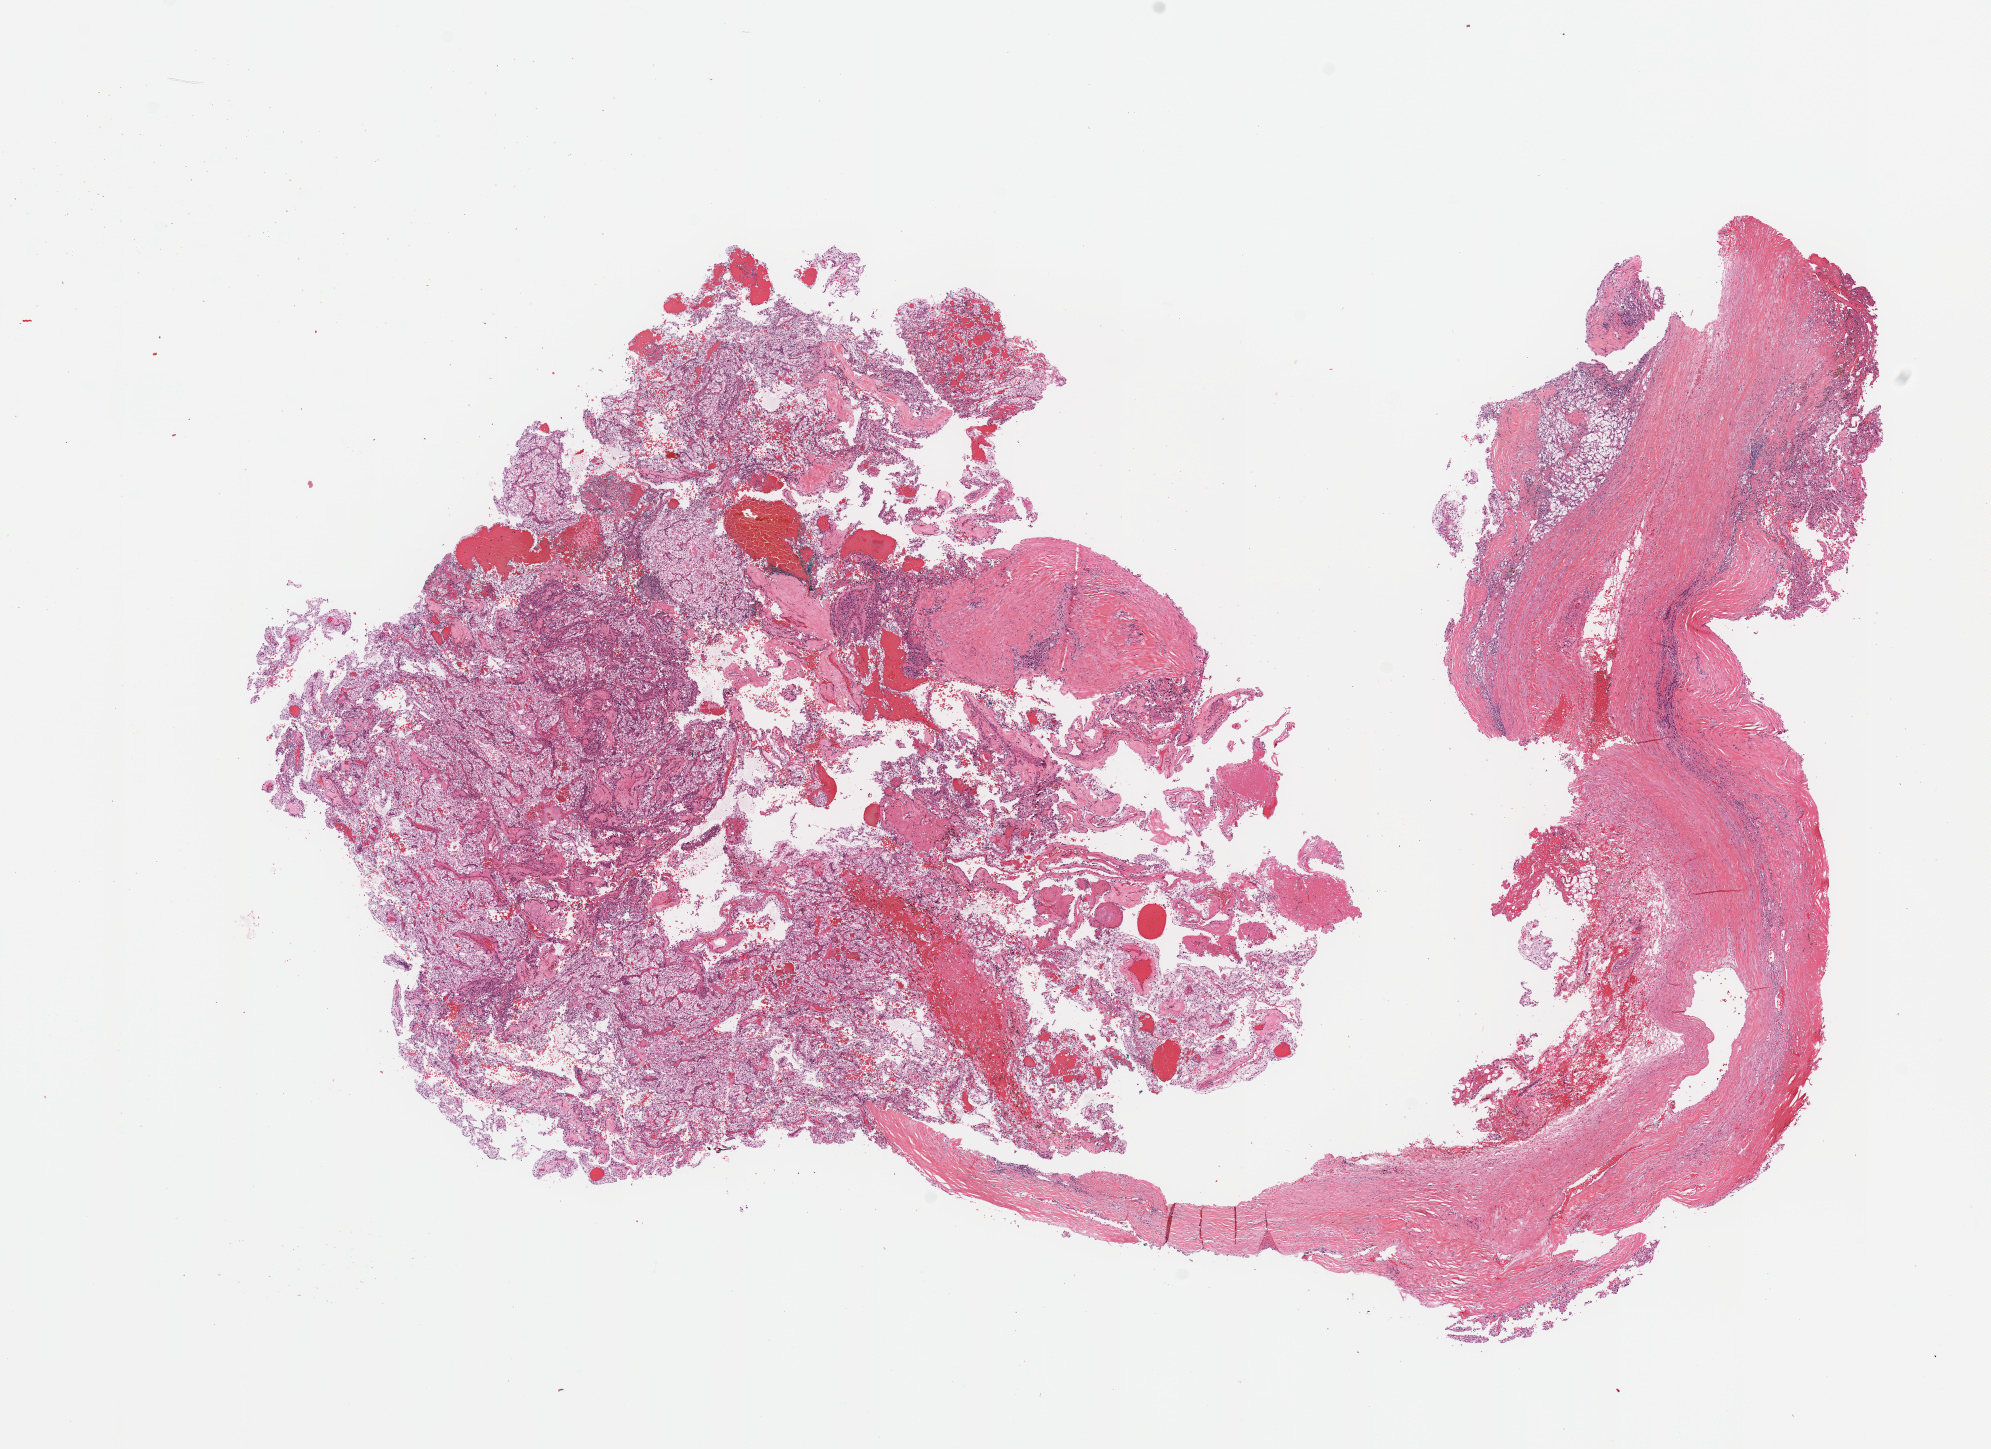
Hematoxylin and eosin (H&E) stained whole-slide image — shown as a low-resolution overview of the whole scanned area (about 15.8 x 11.5 mm). Tumour tissue sample, sampled site: kidney. Patient: male, age 63 years. Histologic grade: G2 (moderately differentiated). Pathologist review of this section (percent, as recorded): tumour nuclei 80%, necrosis 5%.
Primary tumour site (as recorded): lower pole. AJCC pathologic stage: I. Histologic diagnosis: Renal cell carcinoma, NOS.